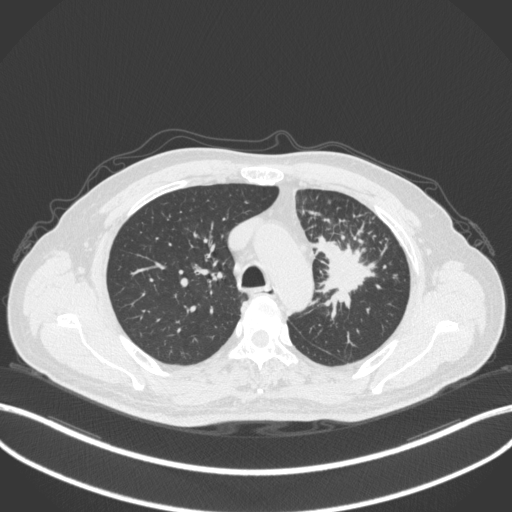
Chest CT, one axial slice. Reconstruction kernel B31f. 120 kVp. Lung window (W 1500 / L -600 HU). 1 mm slice thickness. 512 × 512 image matrix, field of view 400 × 400 mm. Male patient, age 69 years. Case-level facts recorded for this patient, not image findings: clinical TNM (as recorded): T2a N2 M0.
Outlined on this slice (bounding box drawn by a radiologist):
- lung tumour (recorded histology: adenocarcinoma): bounding box (x1, y1, x2, y2) in pixels: (315, 229, 376, 321)